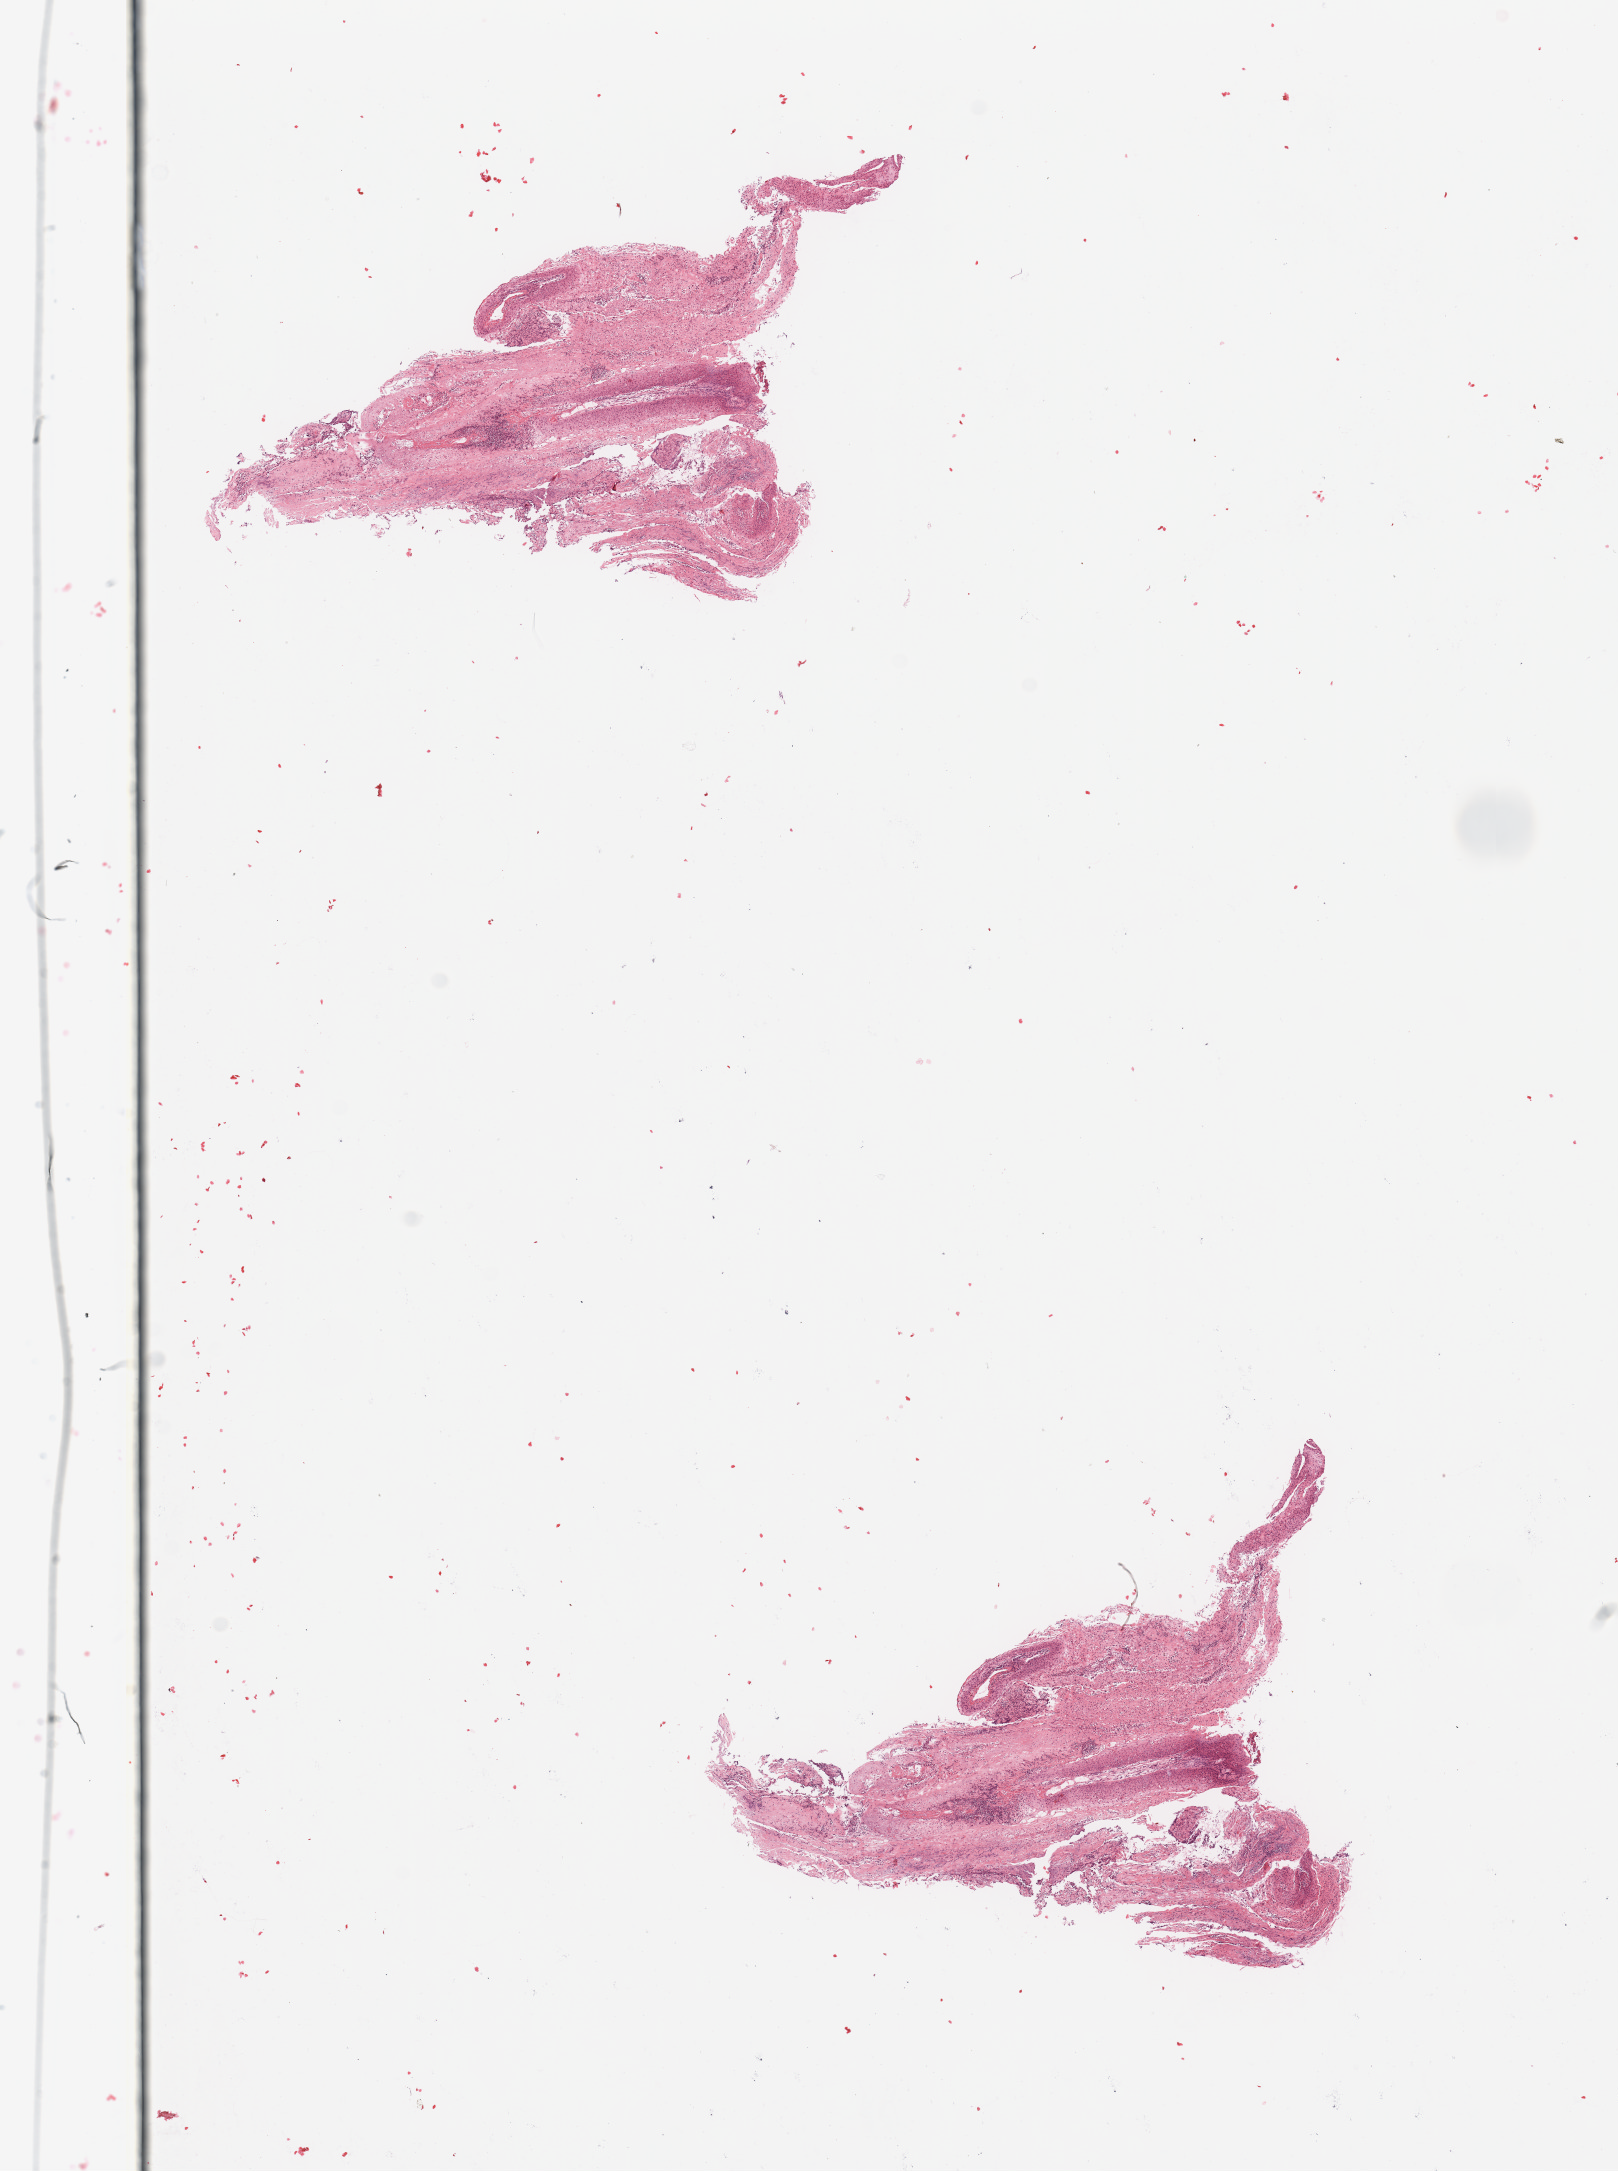
Whole-slide histology image, Hematoxylin and eosin (H&E) stained — whole scanned area (about 12.8 x 17.2 mm, from a 20x scan) shown as a low-resolution overview; tumour tissue sample, sampled site: larynx. Patient: male, age 69 years. Histologic grade: G2 (moderately differentiated). Composition of this section per pathologist review: tumour nuclei 80%, necrosis 10%.
Primary tumour site (as recorded): larynx. AJCC pathologic stage: IVA. Histologic diagnosis: Squamous cell carcinoma, NOS (larynx, NOS).